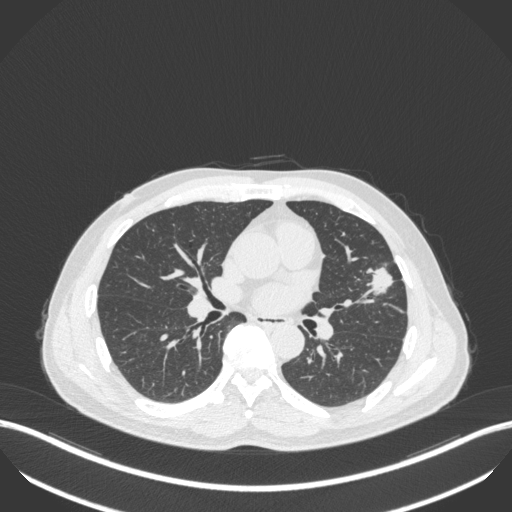
Chest CT, one axial slice; slice 209 of 418 in the series (ordered by position); reconstruction kernel B31f; 120 kVp; lung window (W 1500 / L -600 HU); 1 mm slice thickness; 512 × 512 image matrix, field of view 400 × 400 mm. Male patient, age 55 years. Case-level facts recorded for this patient, not image findings: clinical TNM (as recorded): T1c N0 M0; histopathological grade: G2-3.
Structures marked on this image (bounding box drawn by a radiologist):
- lung tumour (recorded histology: adenocarcinoma): bounding box (x1, y1, x2, y2) in pixels: (365, 265, 395, 299)